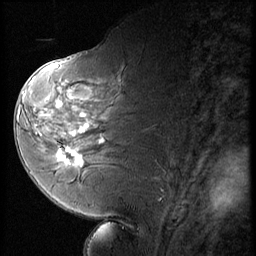
Breast MRI (dynamic contrast-enhanced), one sagittal slice. Position 30 of 56 along the scan axis. 3 images stored at this slice position (order not interpretable as contrast timing). 1.5 T. TE 4.2 ms, TR 9 ms. 2.5 mm slice thickness. 256 × 256 image matrix. Patient: female, 58 years. Case-level facts recorded for this patient, not image findings: setting: breast cancer imaged before/during neoadjuvant chemotherapy; receptor status: HR-positive, HER2-negative.
Outlined on this slice (semi-automatically segmented with operator editing):
- analysis volume of interest (the breast-tissue region the enhancement analysis was run in; not a lesion): bounding box (x1, y1, x2, y2) in pixels: (47, 136, 88, 178)
- tumour enhancement mask (voxels above the 140 % enhancement threshold inside the analysis volume of interest): (56, 149, 82, 164)